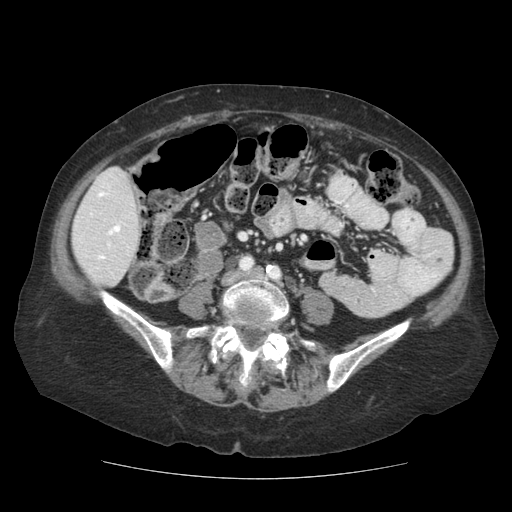
Contrast-enhanced abdominal CT (liver protocol), one axial slice. Position 27 of 111 along the scan axis. Soft-tissue window (W 400 / L 40 HU). 2.5 mm slice thickness. 512 × 512 image matrix, field of view 360 × 360 mm. Case-level facts recorded for this patient, not image findings: diagnosis: hepatocellular carcinoma (patient treated with transarterial chemoembolisation; whether this scan precedes or follows treatment is not stated here); TNM stage (as recorded): Stage-I; Child-Pugh class: A.
Annotated regions visible in this slice (semi-automatically segmented with operator editing):
- liver parenchyma outside the tumour (the mass and vessels are separate outlines, so this box may not span the whole liver): bounding box (x1, y1, x2, y2) in pixels: (72, 167, 140, 286)
- liver vessels: (91, 191, 121, 259)